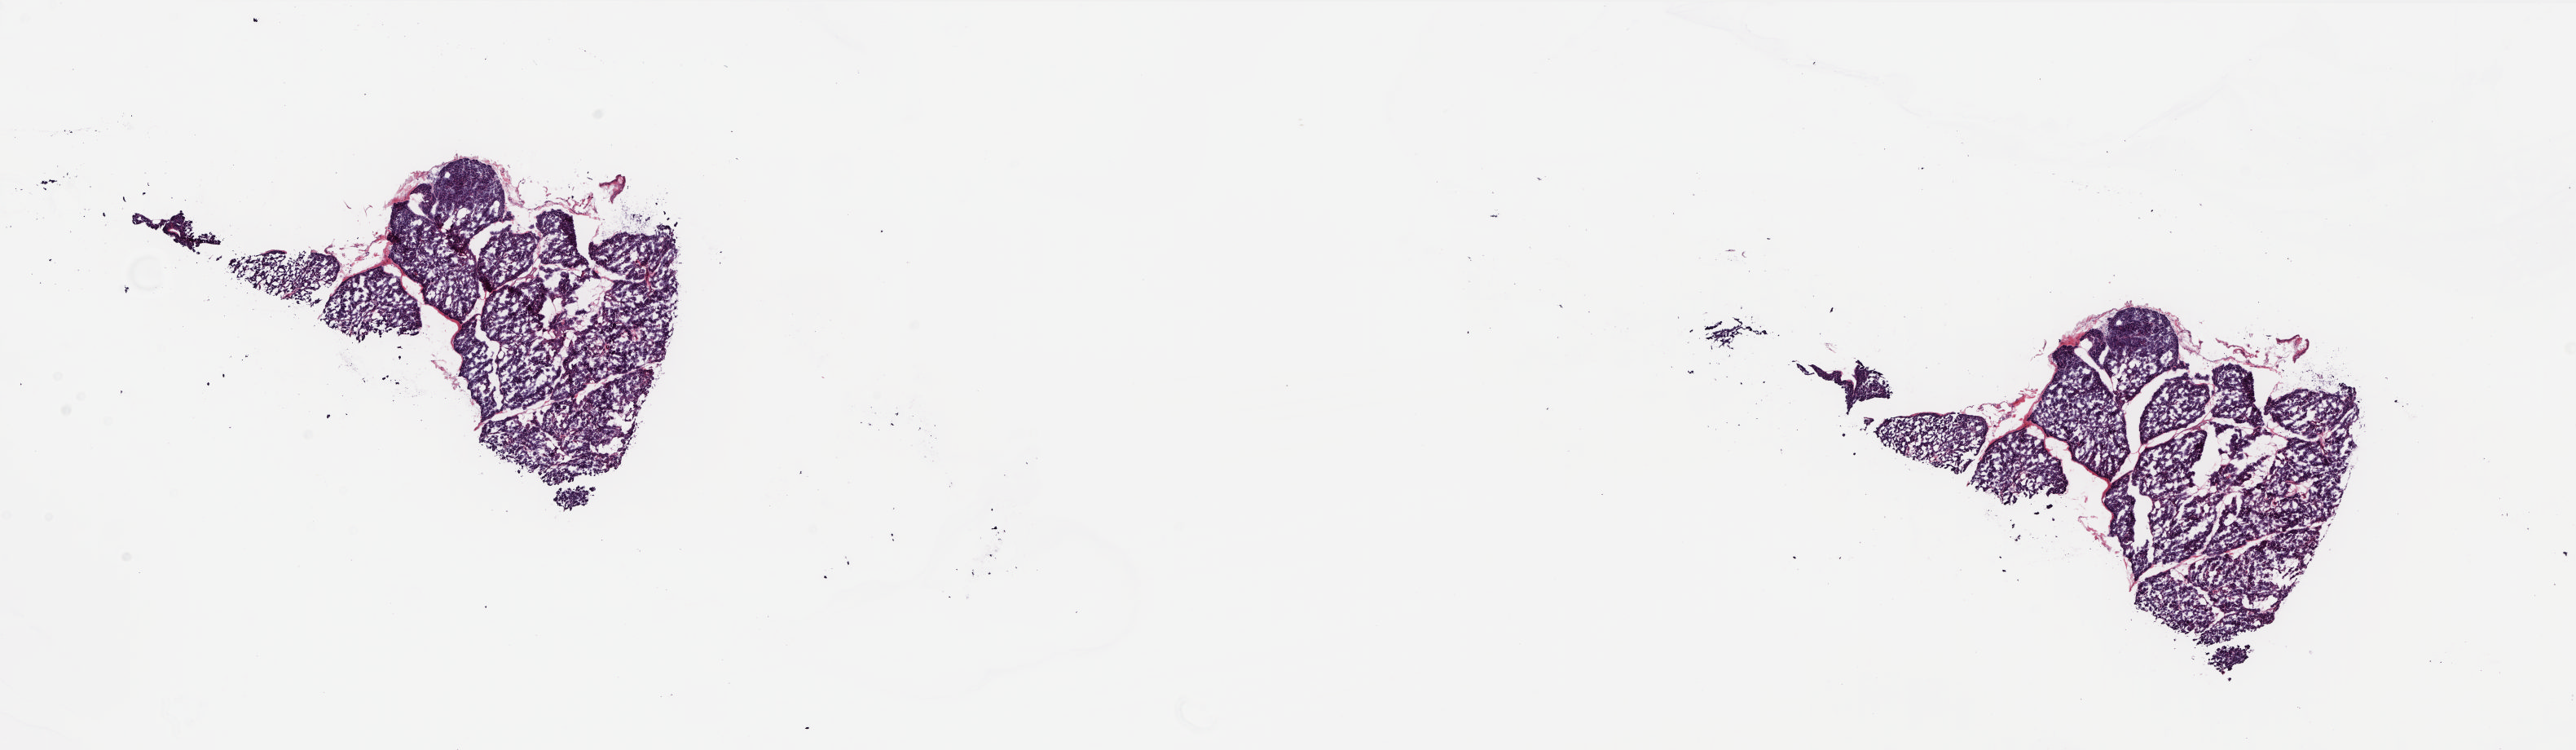
H&E whole-slide image, low-resolution overview of the scanned area, about 25.5 x 7.4 mm; frozen section from the top of the tissue portion; sample: solid tissue normal (non-tumour tissue), retroperitoneum and peritoneum. Female, age 60 years at initial diagnosis. Slide review estimates, as recorded: tumour cells 0%, tumour nuclei 0%, normal cells 100%, stromal cells 0%, necrosis 0%. Inflammatory infiltration, as recorded: lymphocyte infiltration 1%, monocyte infiltration 0%, neutrophil infiltration 0%.
* this section: solid tissue normal sample (biorepository sample class)
* patient diagnosis: Dedifferentiated liposarcoma